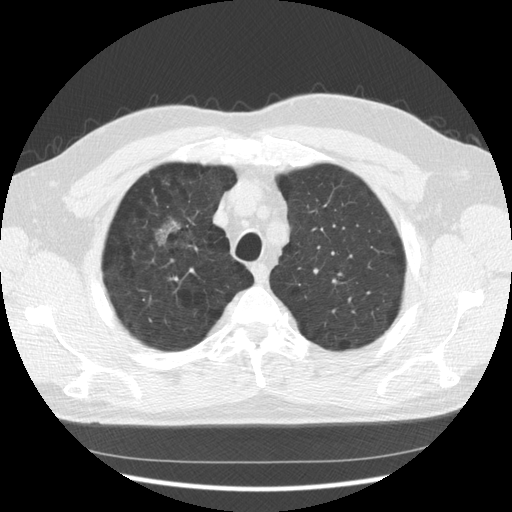
Low-dose screening chest CT, one axial slice. Position 101 of 133 along the scan axis. 140 kVp. Lung window (W 1500 / L -600 HU). 2.5 mm slice thickness. 512 × 512 image matrix.
Annotated regions visible in this slice (expert manual segmentation):
- lesion 1 (tumor, upper lobe of right lung): bounding box (x1, y1, x2, y2) in pixels: (156, 220, 180, 245)